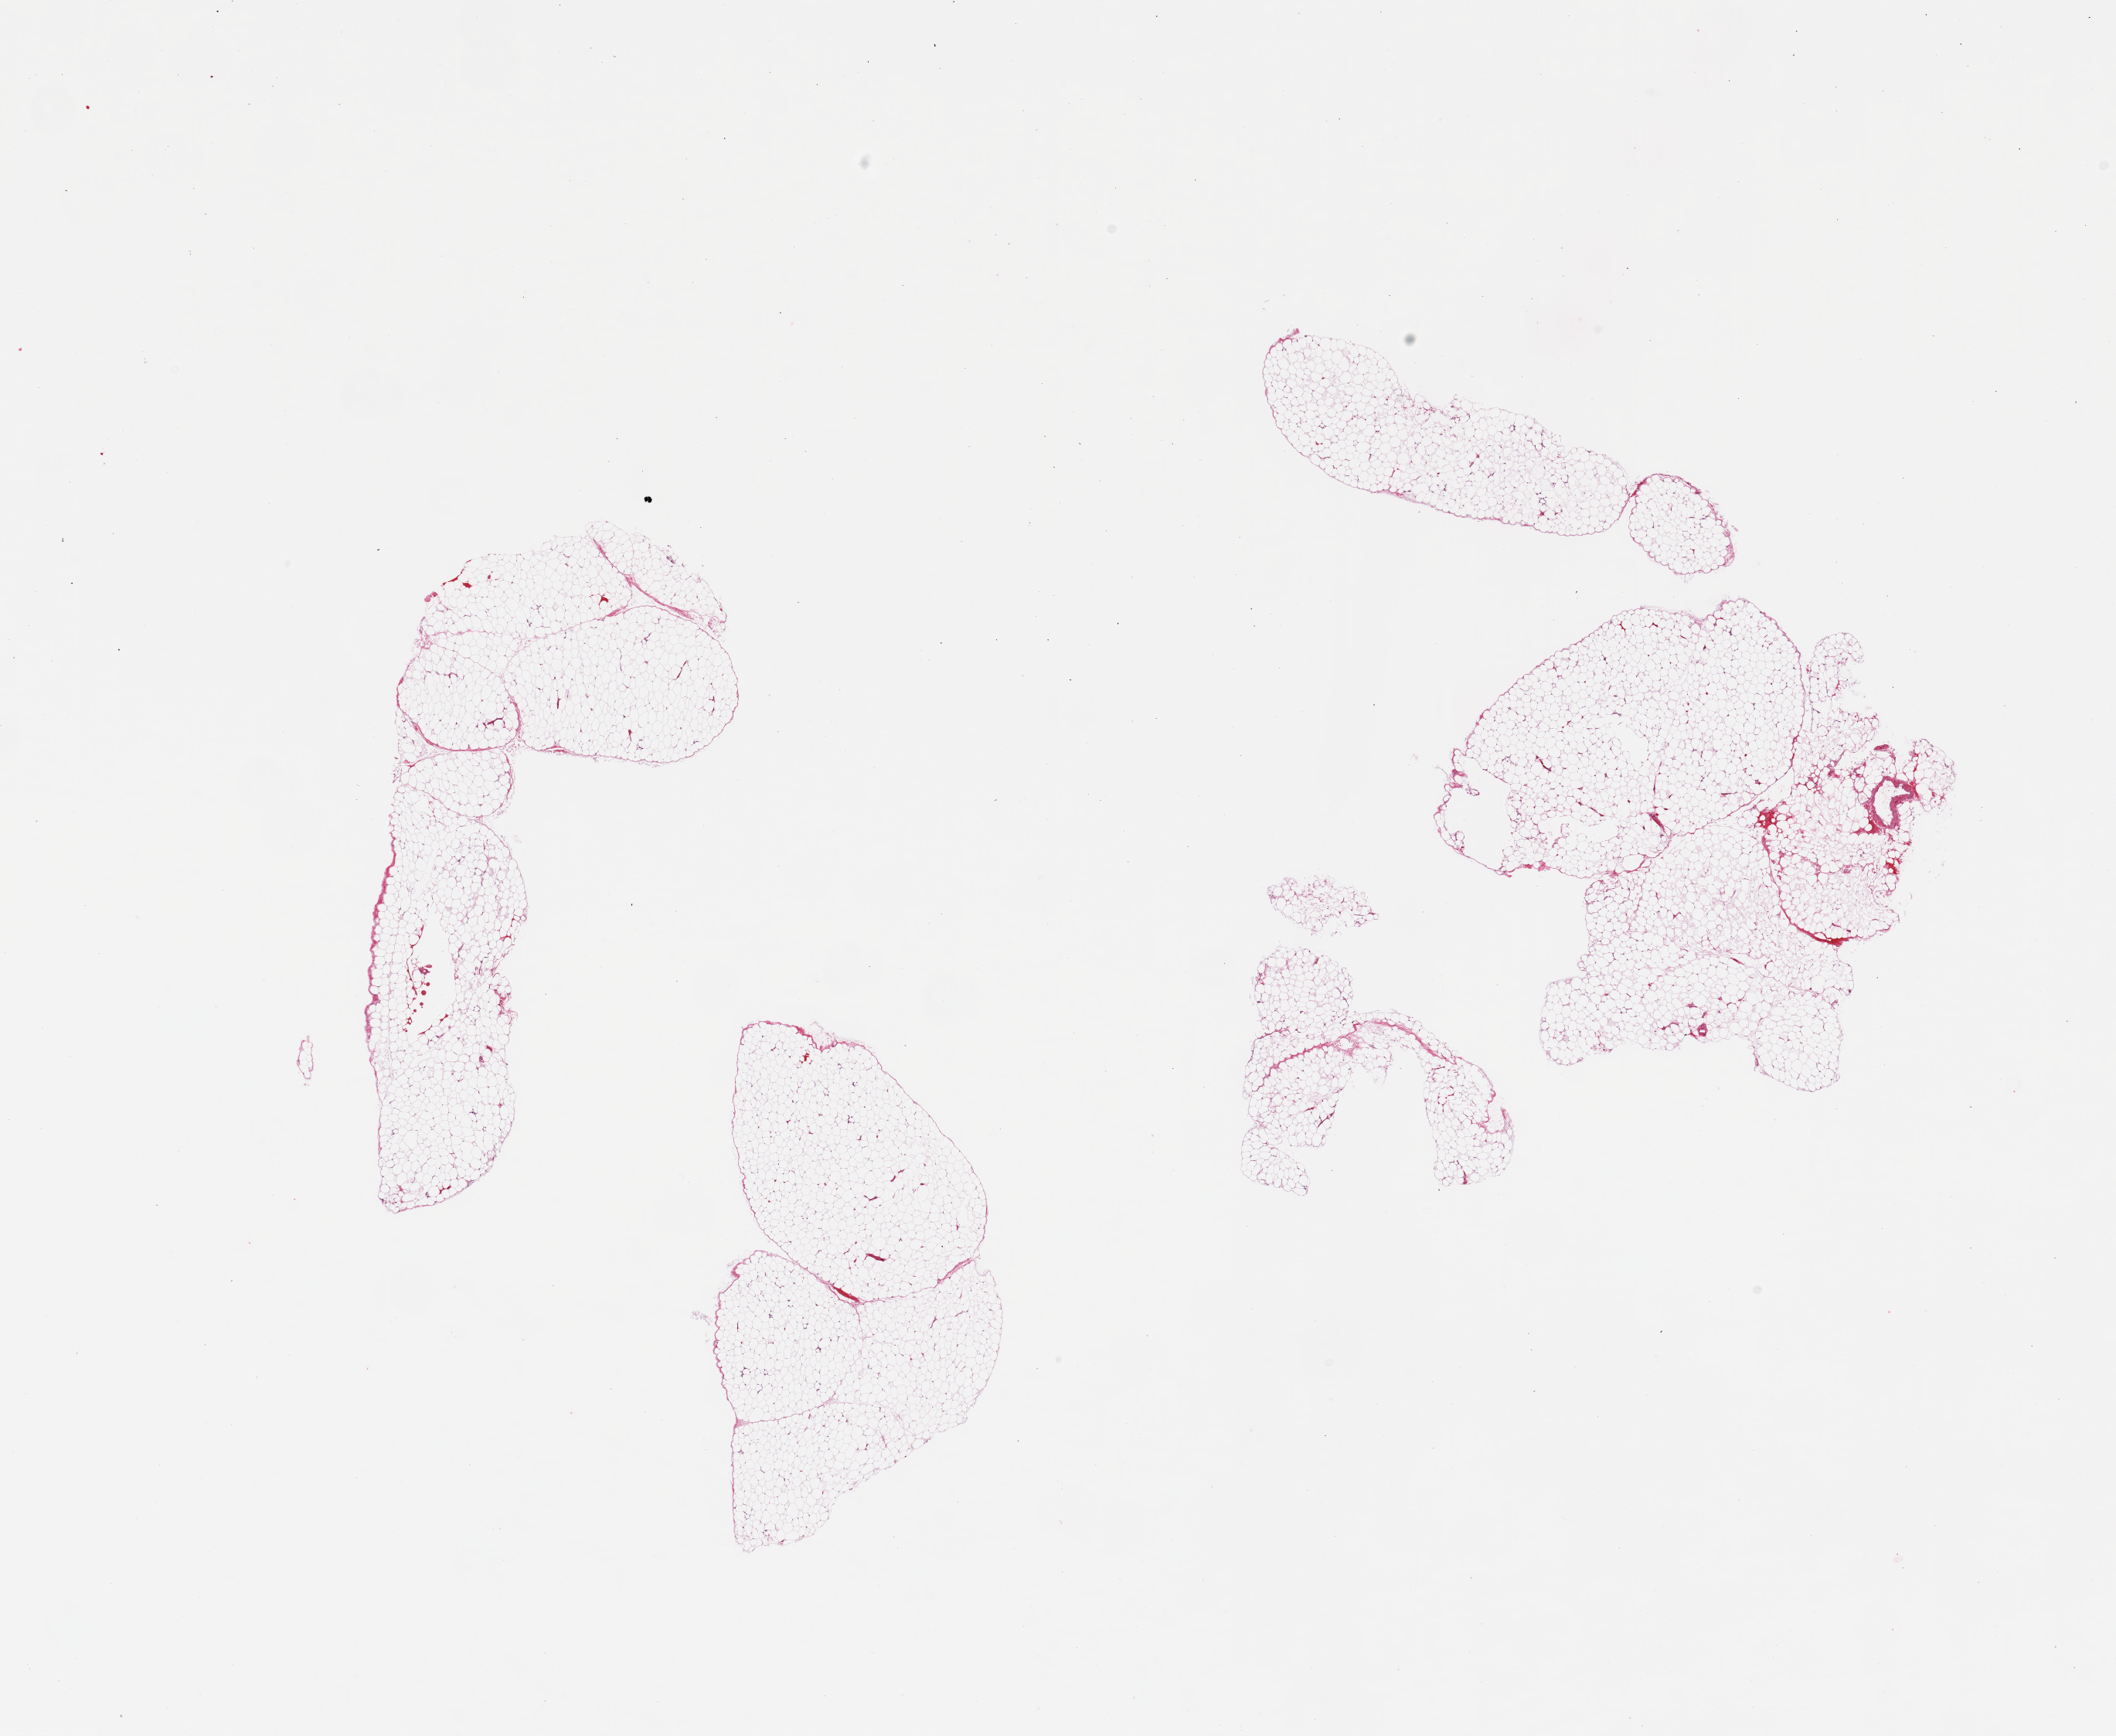
Whole-slide image, H&E stain, brightfield, a low-resolution overview of the entire scanned area, about 21.7 x 17.8 mm (slide scanned at 20x), PAXgene-fixed paraffin-embedded (PFPE) section, sampled site (target tissue): omentum, tissue donor sample. Donor: male.
Reviewer comment on this tissue sample: 2 pieces, trace mesothelium fascia.